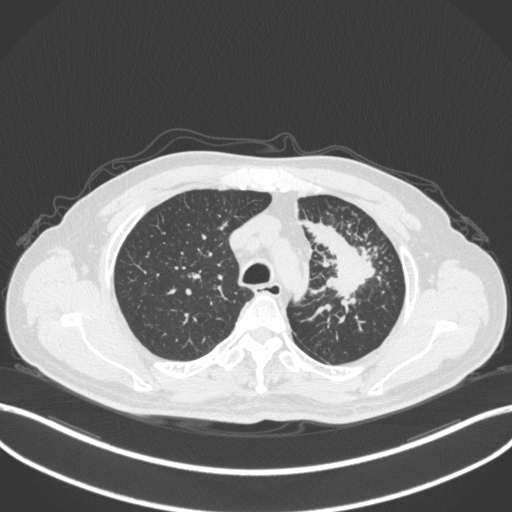
Chest CT, one axial slice; slice 275 of 386 in the series (ordered by position); reconstruction kernel B31f; lung window (W 1500 / L -600 HU); 512 × 512 image matrix, field of view 400 × 400 mm. Patient: male, 69 years. Case-level facts recorded for this patient, not image findings: clinical TNM (as recorded): T2a N2 M0.
Structures marked on this image (bounding box drawn by a radiologist):
- lung tumour (recorded histology: adenocarcinoma): bounding box [x1, y1, x2, y2] px = [298, 217, 385, 304]